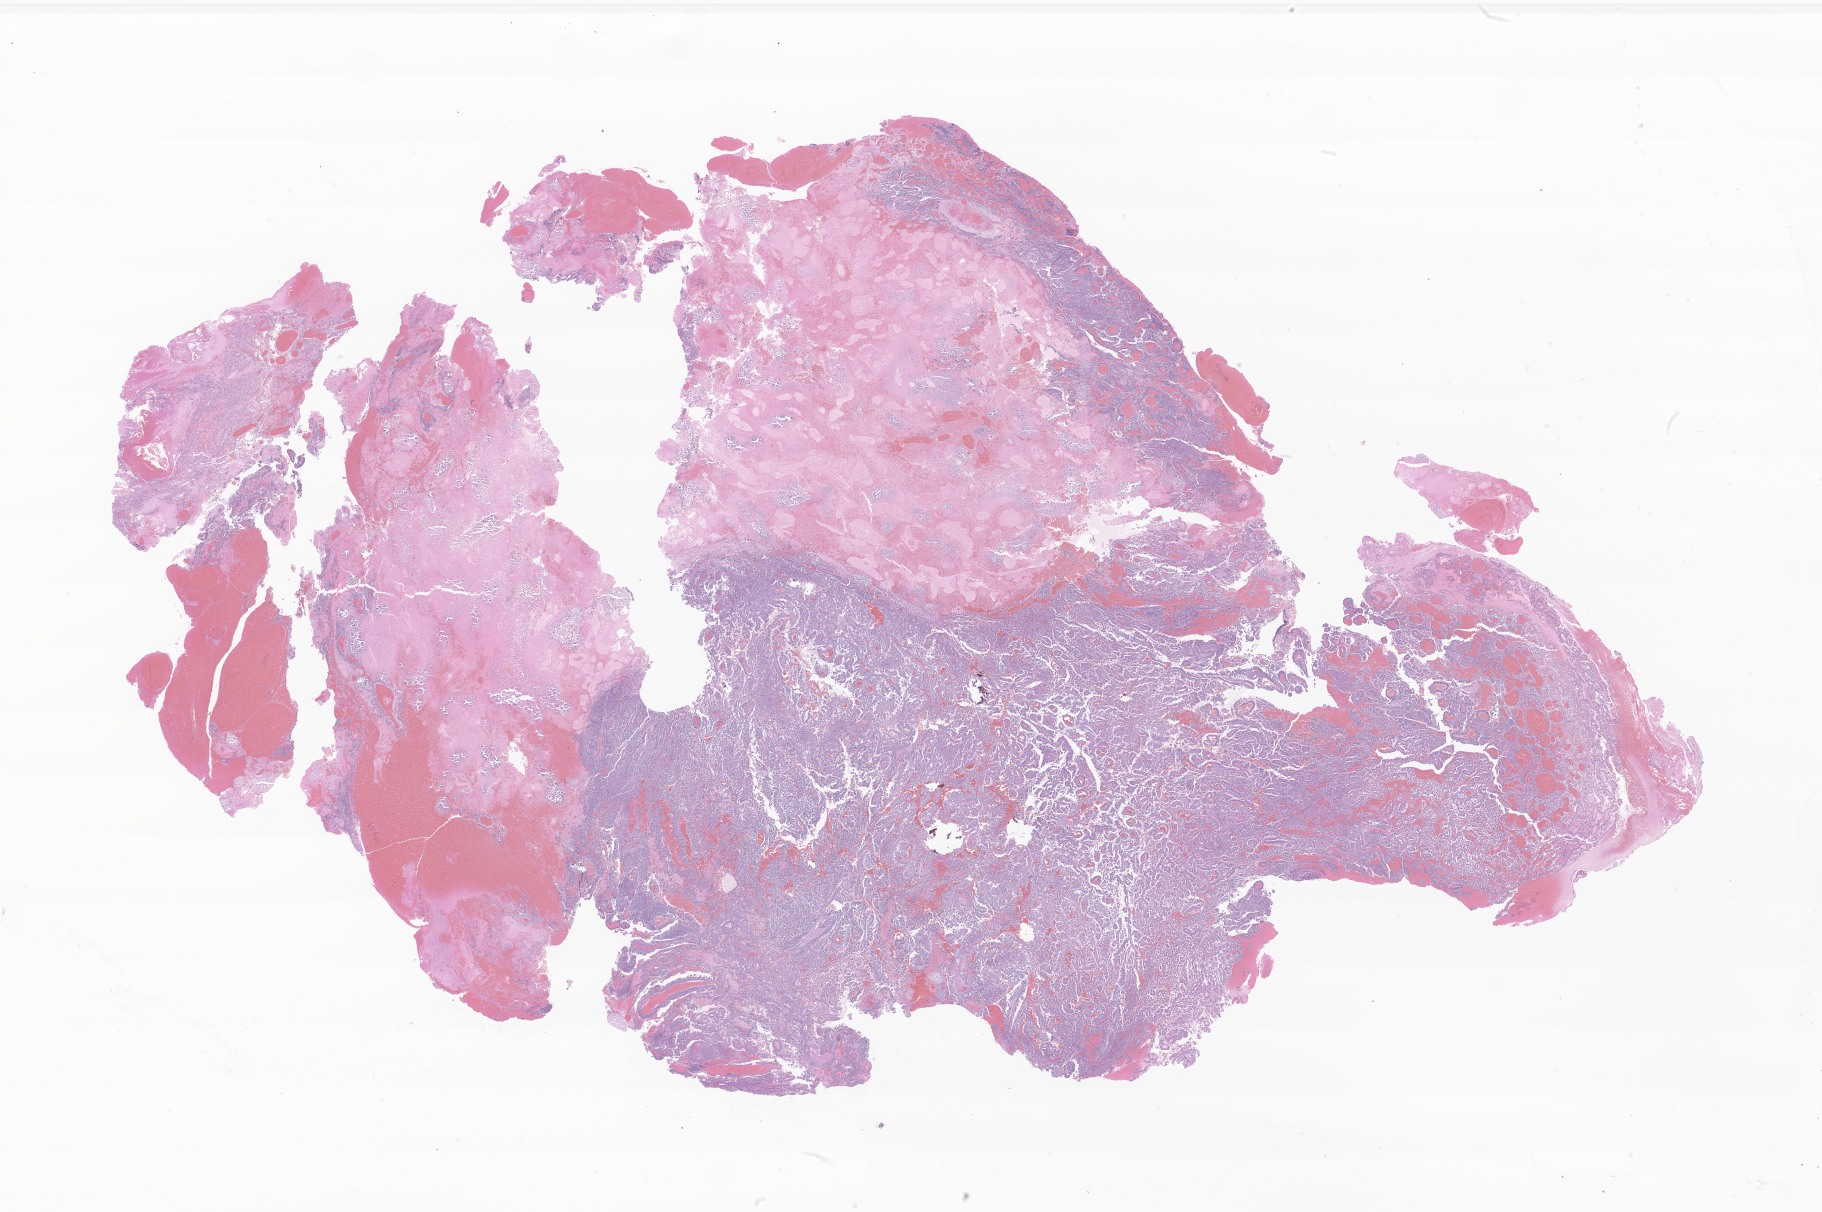
Digitized hematoxylin and eosin (H&E)-stained section of tumor tissue from the brain, shown as a low-resolution overview of the whole scanned area (about 30.7 x 20.4 mm); formalin-fixed paraffin-embedded section. Patient male; age 892 days (about 2.4 years).
Diagnosis (ICD-O-3 morphology term): Choroid plexus carcinoma.